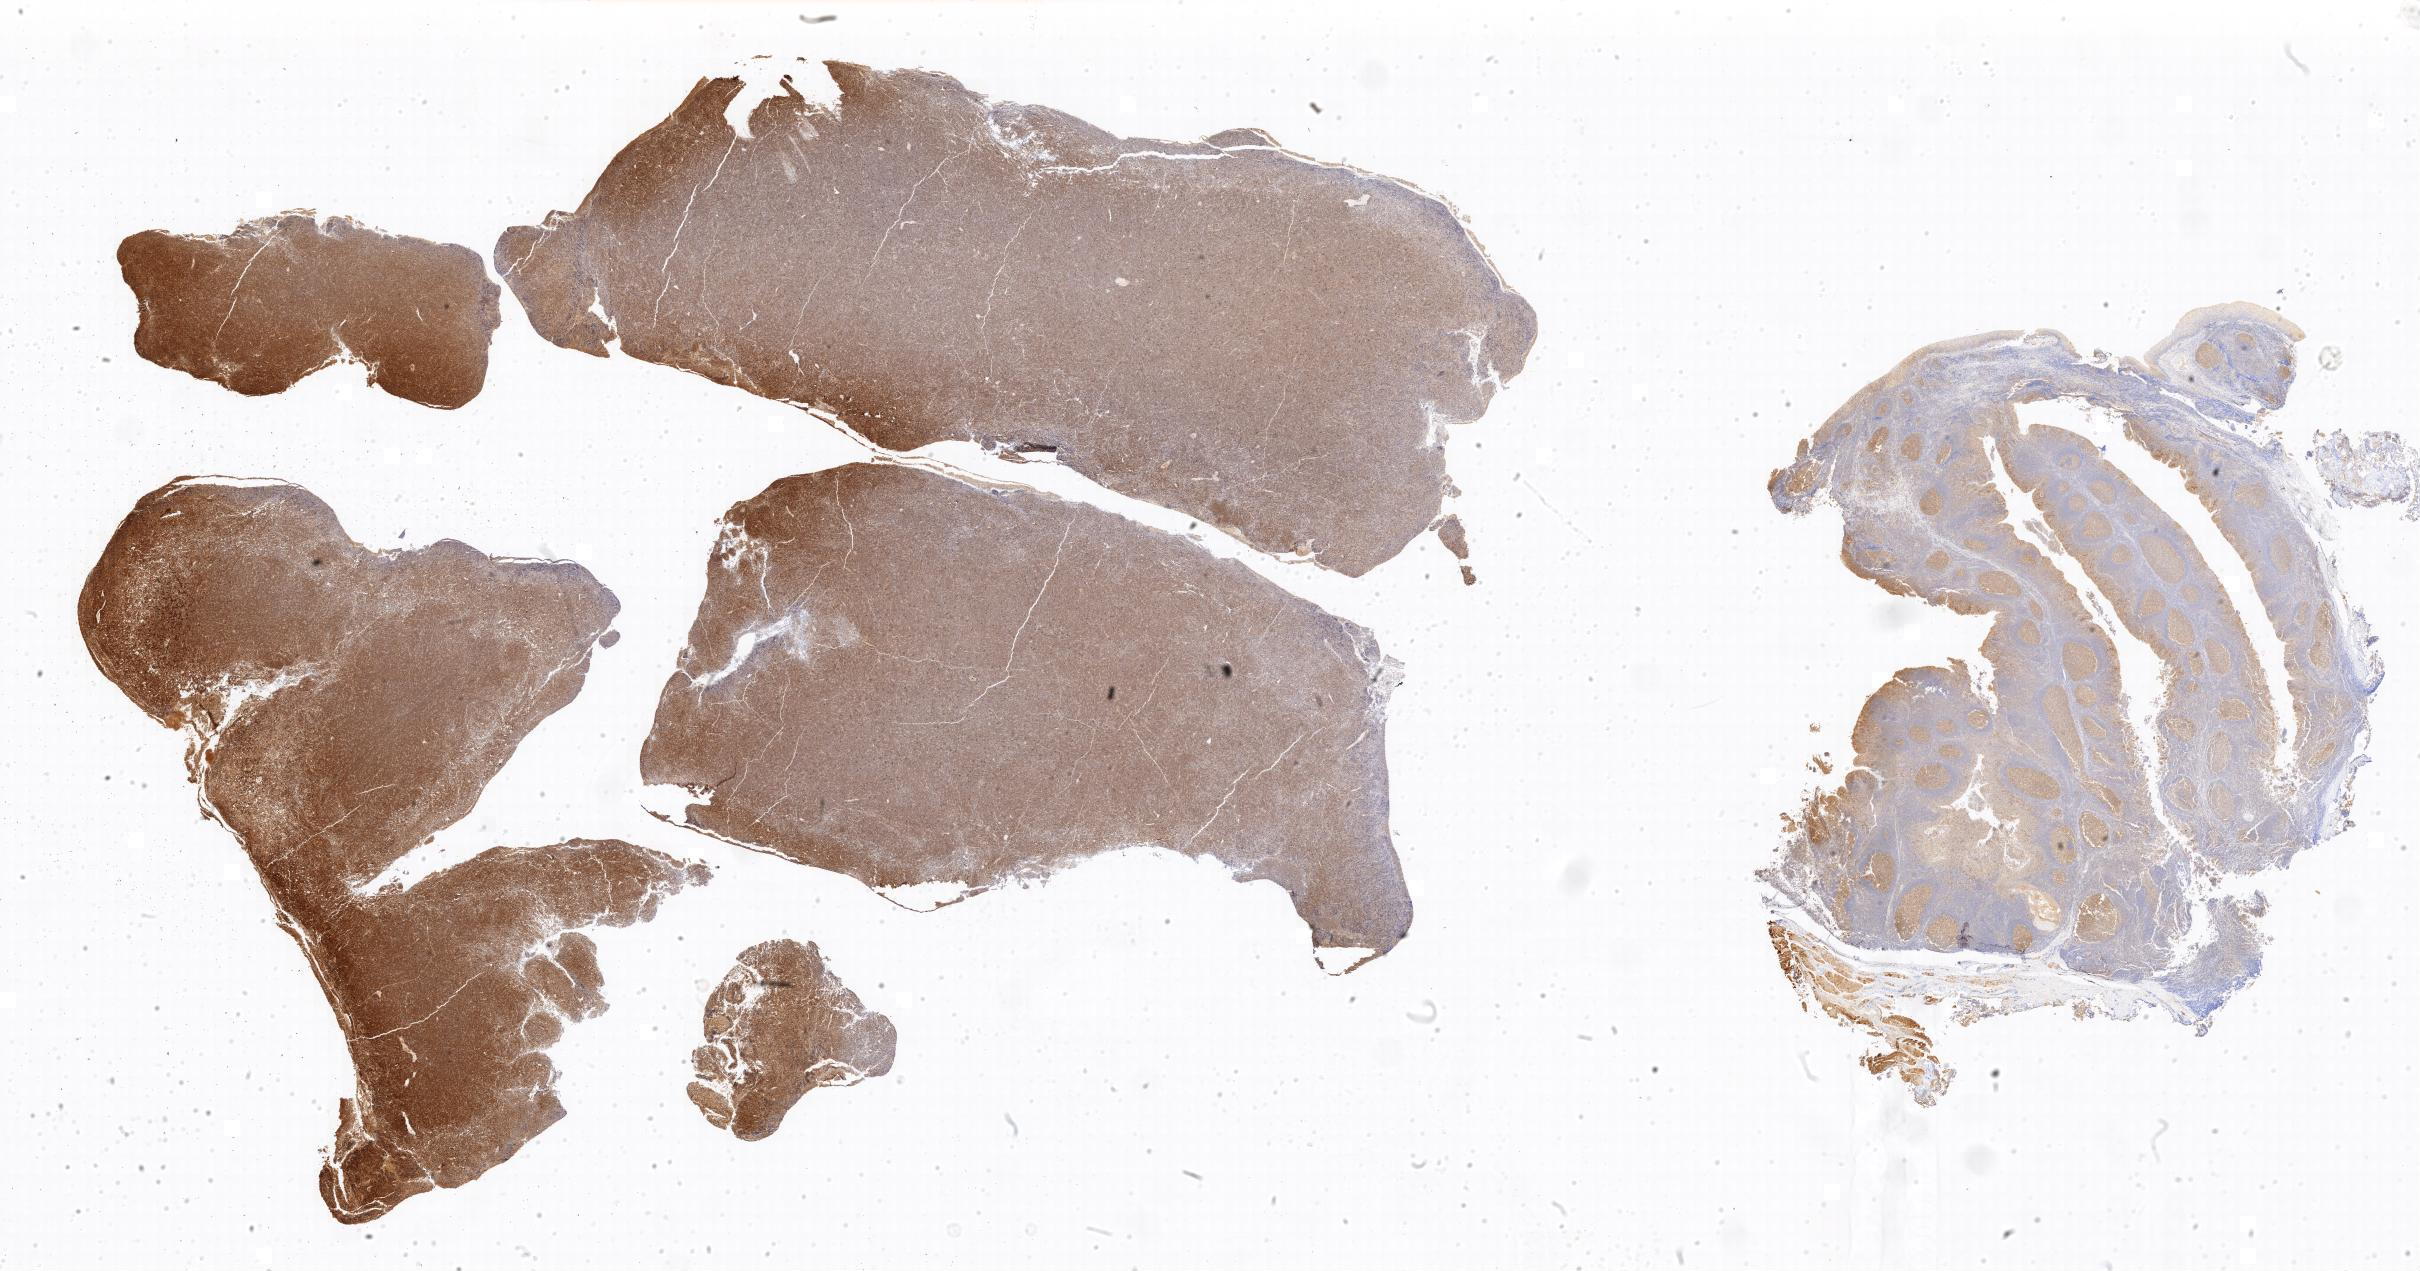
IHC for BCL6, whole-slide image — low-resolution overview of the scanned area, tumor tissue, site: peritoneum. Female, age 7 years at initial diagnosis.
- histologic diagnosis: Burkitt lymphoma, NOS